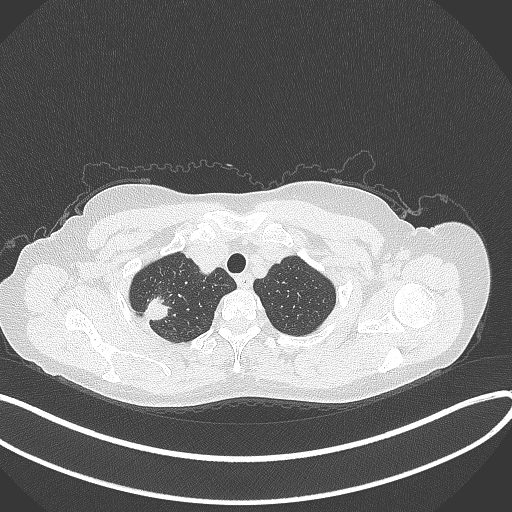
Chest CT, one axial slice; position 321 of 337 along the scan axis; 120 kVp; lung window (W 1500 / L -600 HU); 512 × 512 image matrix, field of view 400 × 400 mm. Female patient, age 50 years. From the clinical record (not read from this slice): clinical TNM (as recorded): T1c N0 M0; histopathological grade: G2-3.
Outlined on this slice (rectangle marked by the reading radiologist):
- lung tumour (recorded histology: adenocarcinoma): box from (x=136, y=293) to (x=175, y=323) px